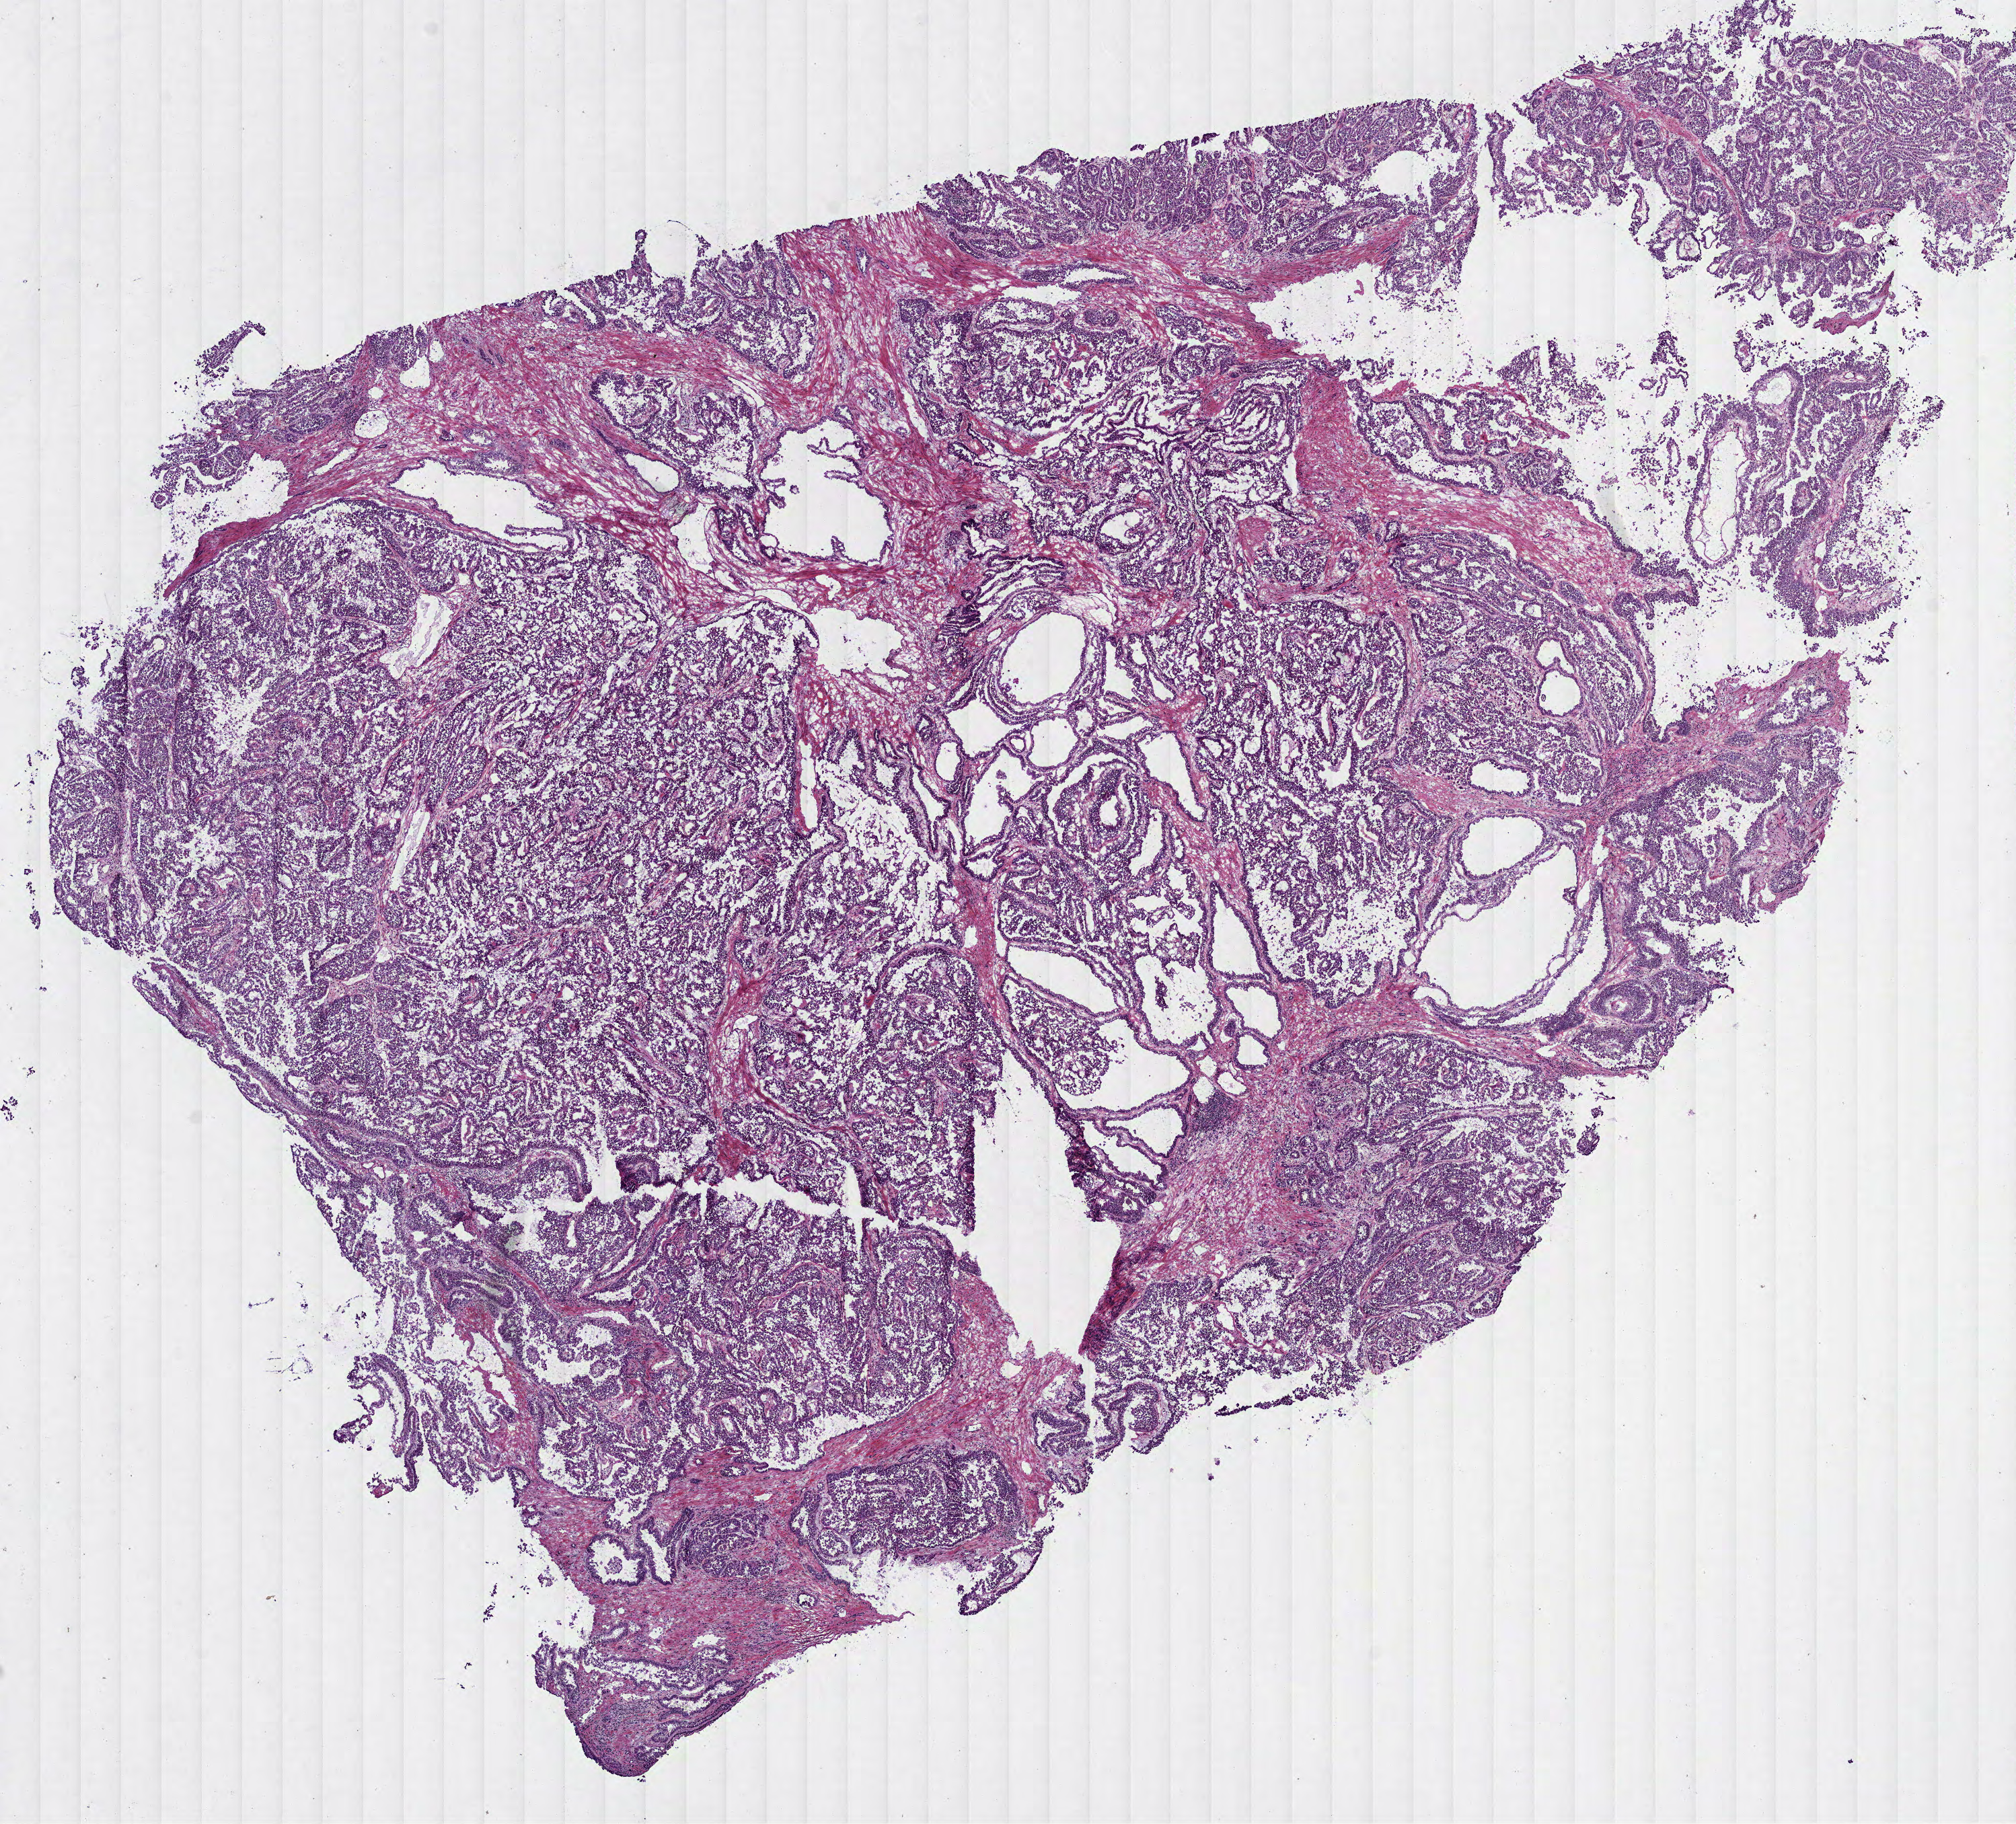
Whole-slide histology image, H&E-stained, low-resolution overview of the scanned area, about 12.1 x 10.9 mm, frozen section from the bottom of the tissue portion, sample: primary tumour, kidney. Patient: male, age at initial diagnosis 61 years.
Histologic diagnosis: Papillary adenocarcinoma, NOS.